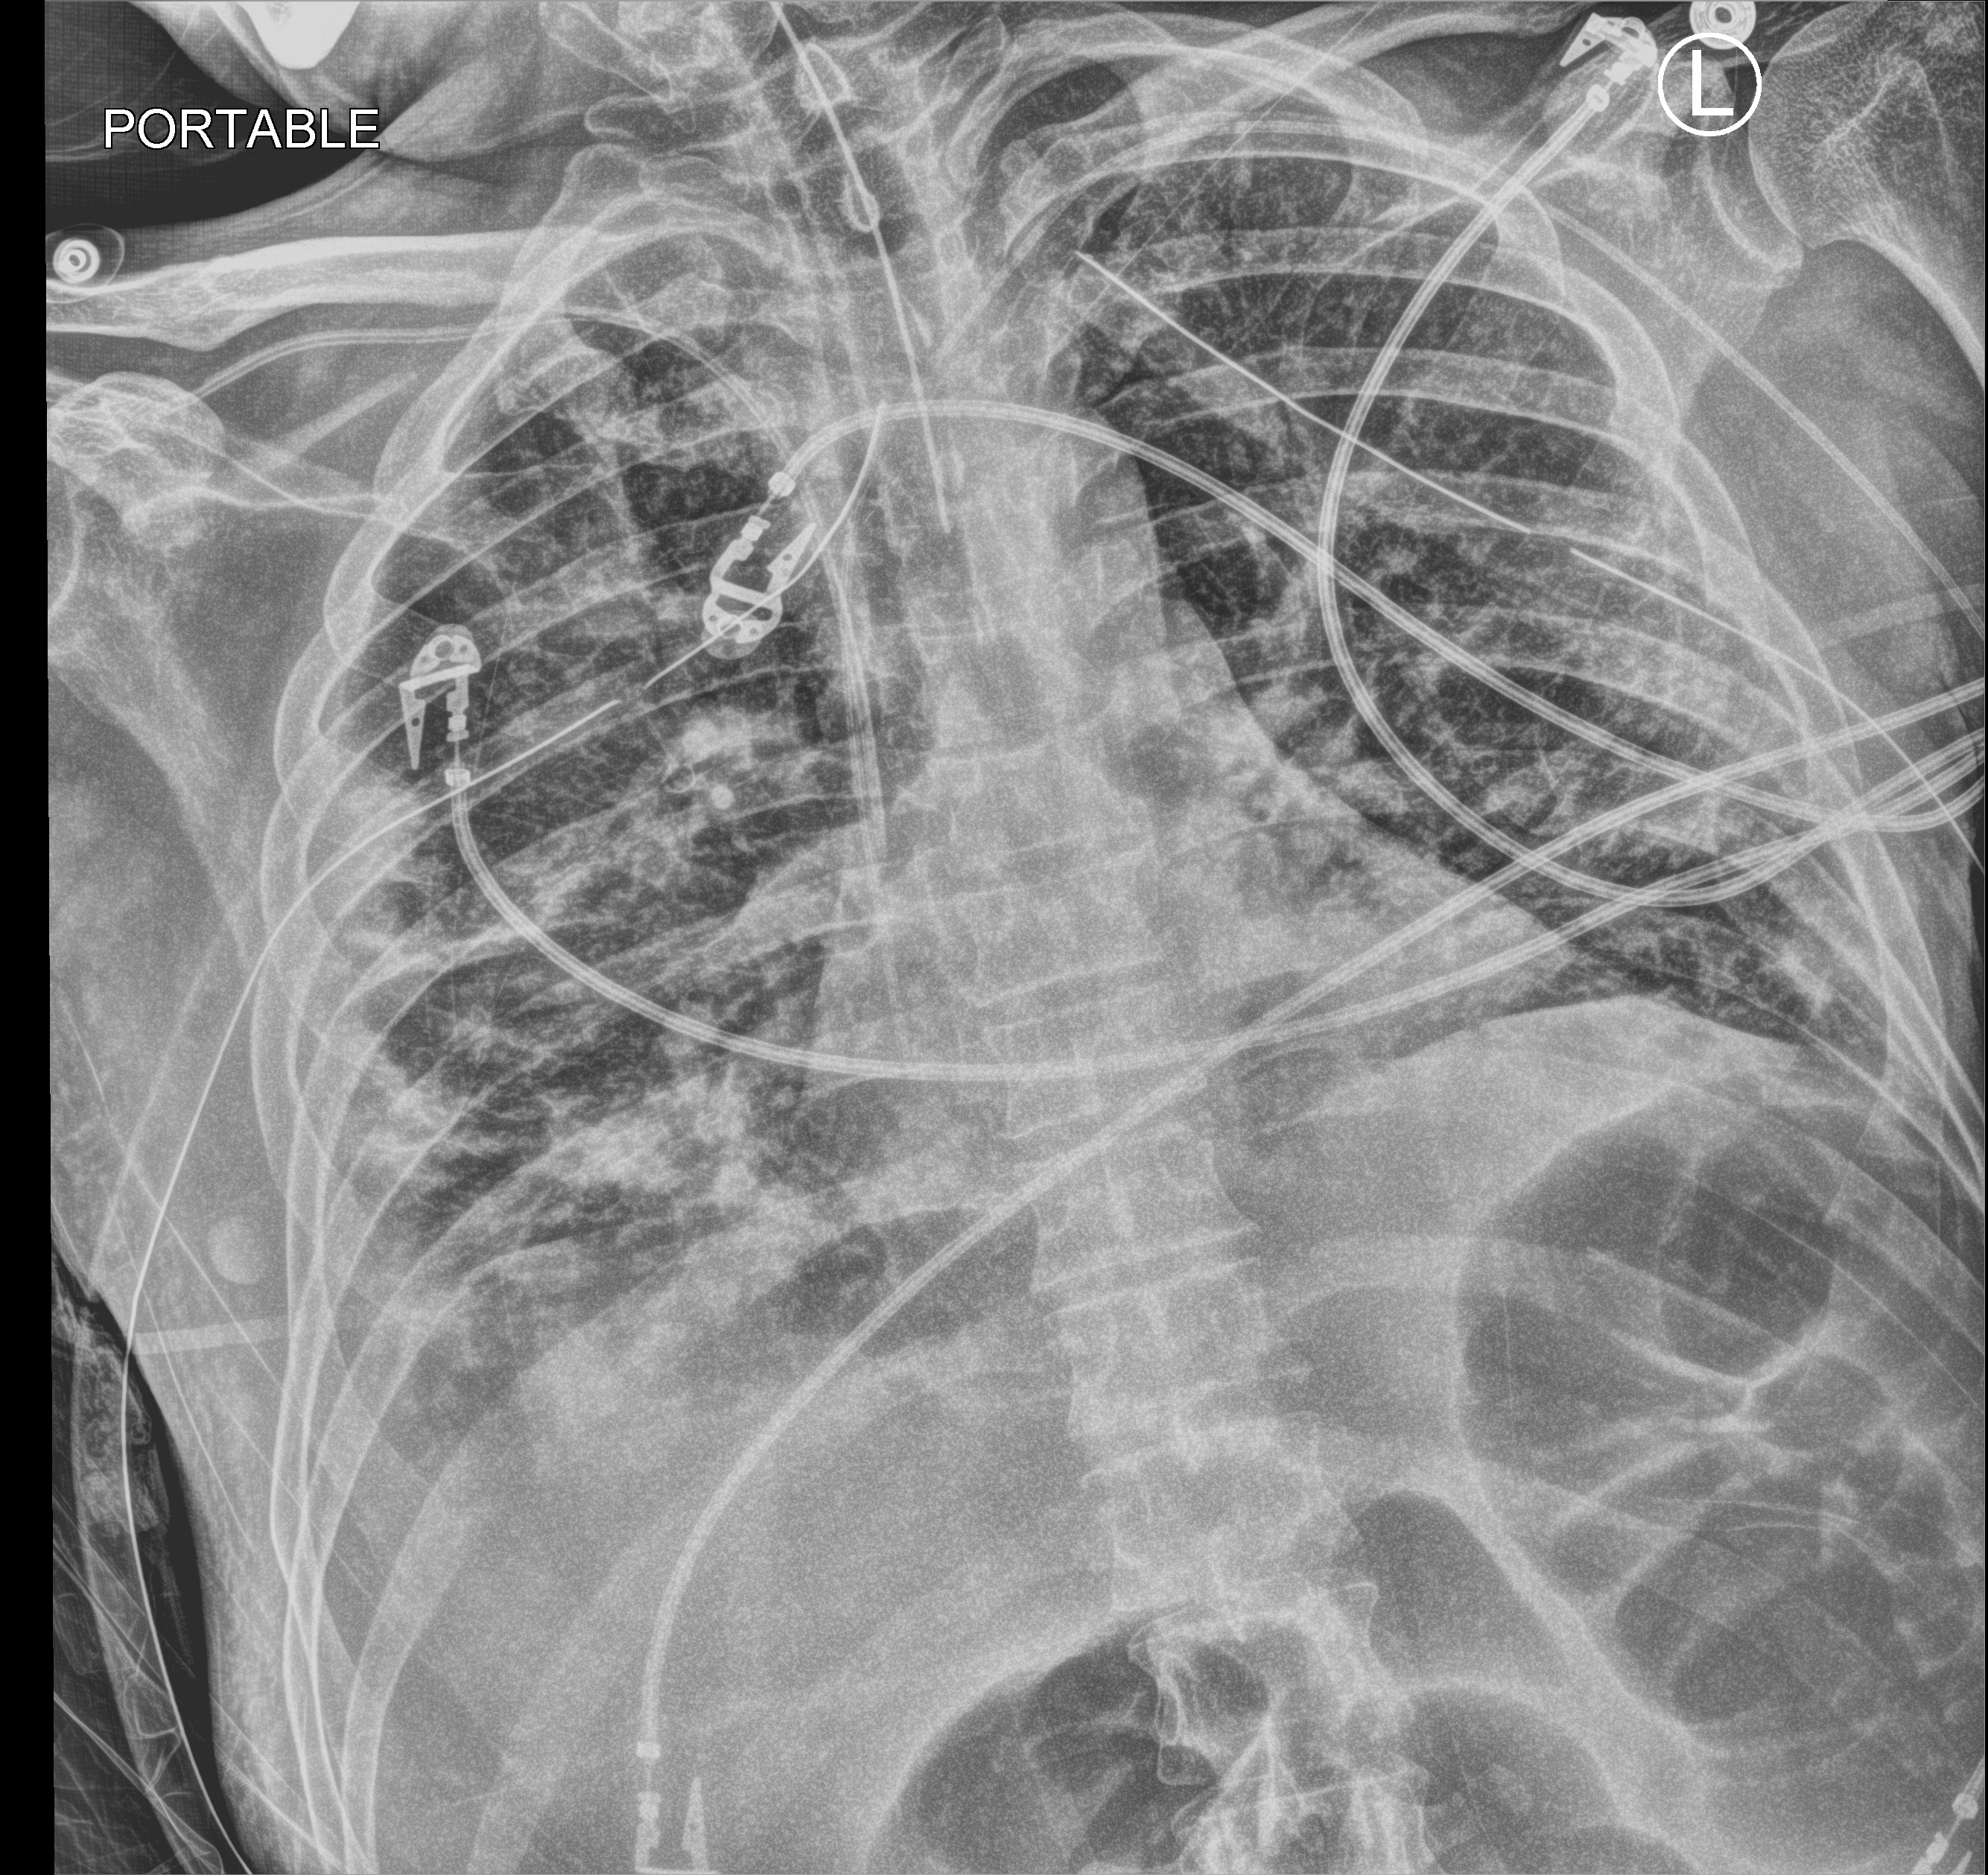
Portable chest radiograph; anteroposterior (AP) projection. Patient hospitalised with COVID-19; male, aged 18–59 years.
Hospital-stay facts (about this admission, not read from this image; timing relative to this image not recorded): smoking status (admission record): never; diabetes (admission record): yes; mechanically ventilated during this hospital stay: yes.